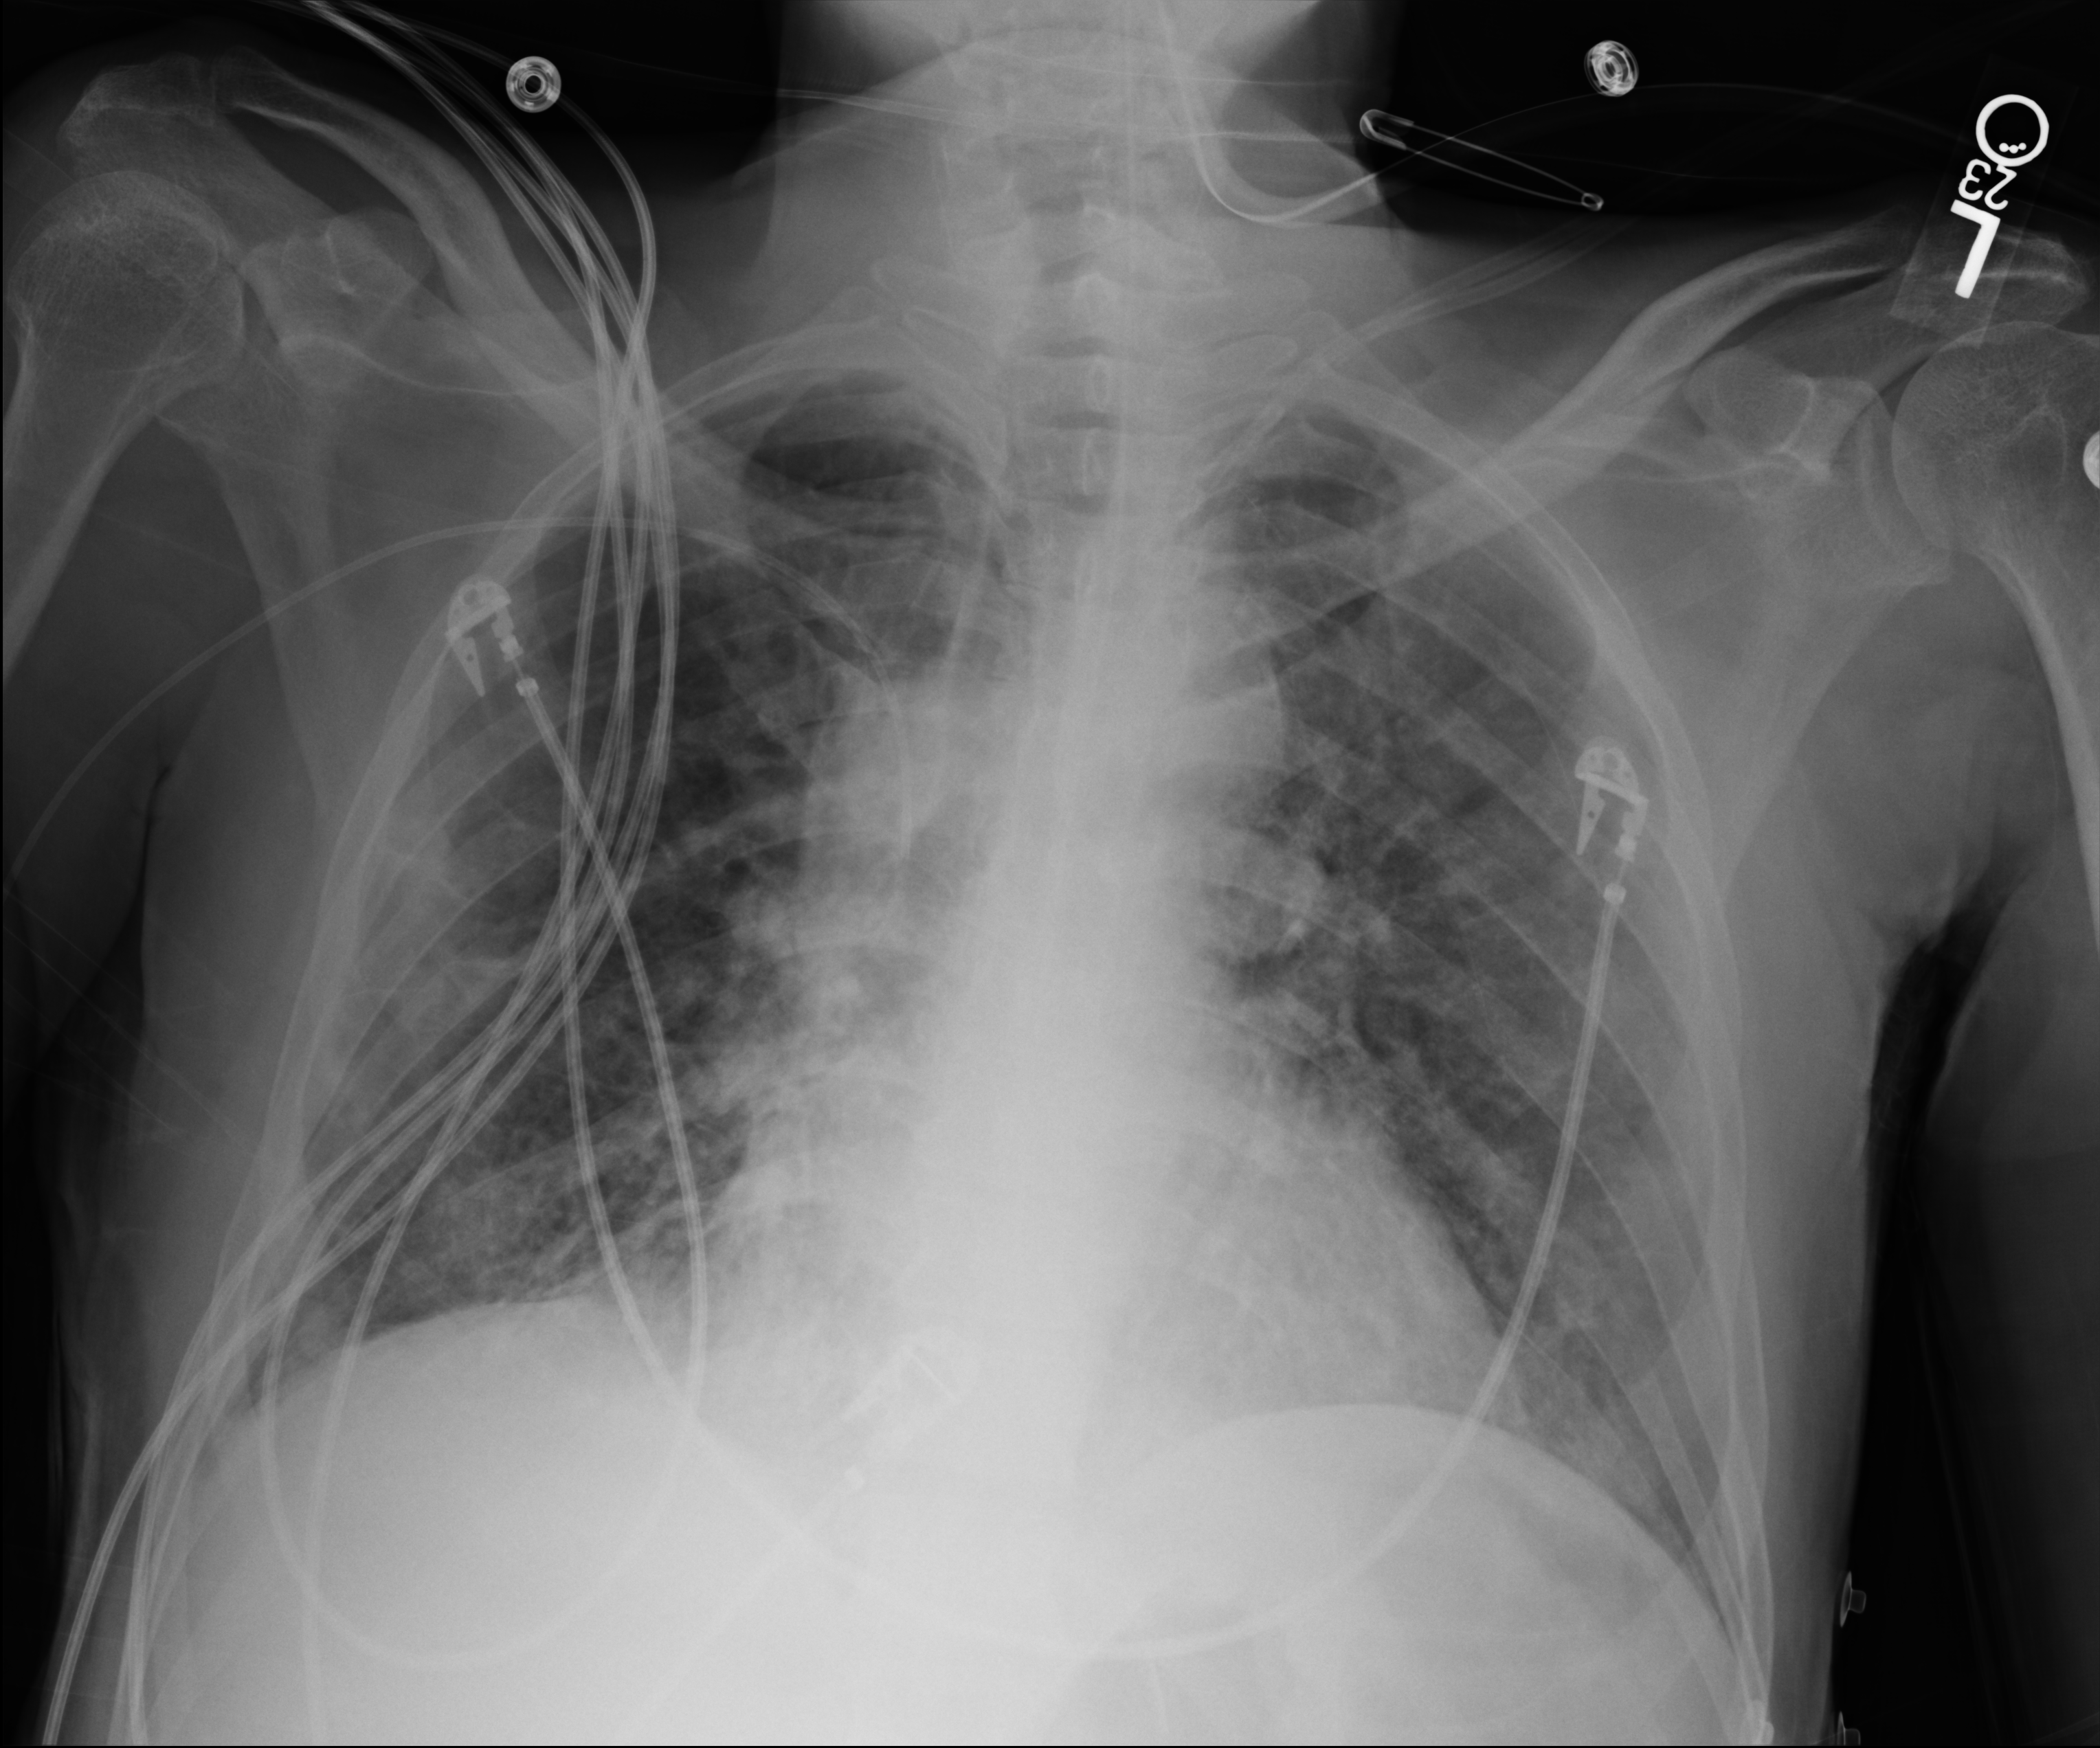
Portable chest radiograph; anteroposterior (AP) projection. Patient hospitalised with COVID-19; male, aged 18–59 years.
Admission-level facts for this patient (not findings on this image; timing relative to this image not recorded):
- mechanically ventilated during this hospital stay: yes